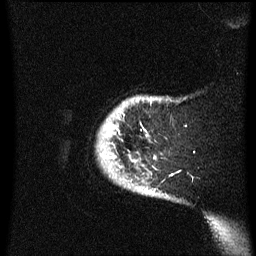
Breast MRI (dynamic contrast-enhanced), one sagittal slice. Position 55 of 60 along the scan axis. Dynamic contrast-enhanced series, image 2 of 3 at this slice position (ordered by acquisition). 1.5 T. TE 4.2 ms, TR 8.4 ms. 2.3 mm slice thickness. 256 × 256 image matrix, field of view 200 × 200 mm. Patient: female, 38 years. From the clinical record (not read from this slice): setting: breast cancer imaged before/during neoadjuvant chemotherapy; receptor status: HER2-positive.
Outlined on this slice (semi-automatically segmented with operator editing):
- analysis volume of interest (the breast-tissue region the enhancement analysis was run in; not a lesion): box from (x=97, y=96) to (x=173, y=199) px
- tumour enhancement mask (voxels above the 70 % enhancement threshold inside the analysis volume of interest): (x=109, y=126)–(x=119, y=135)